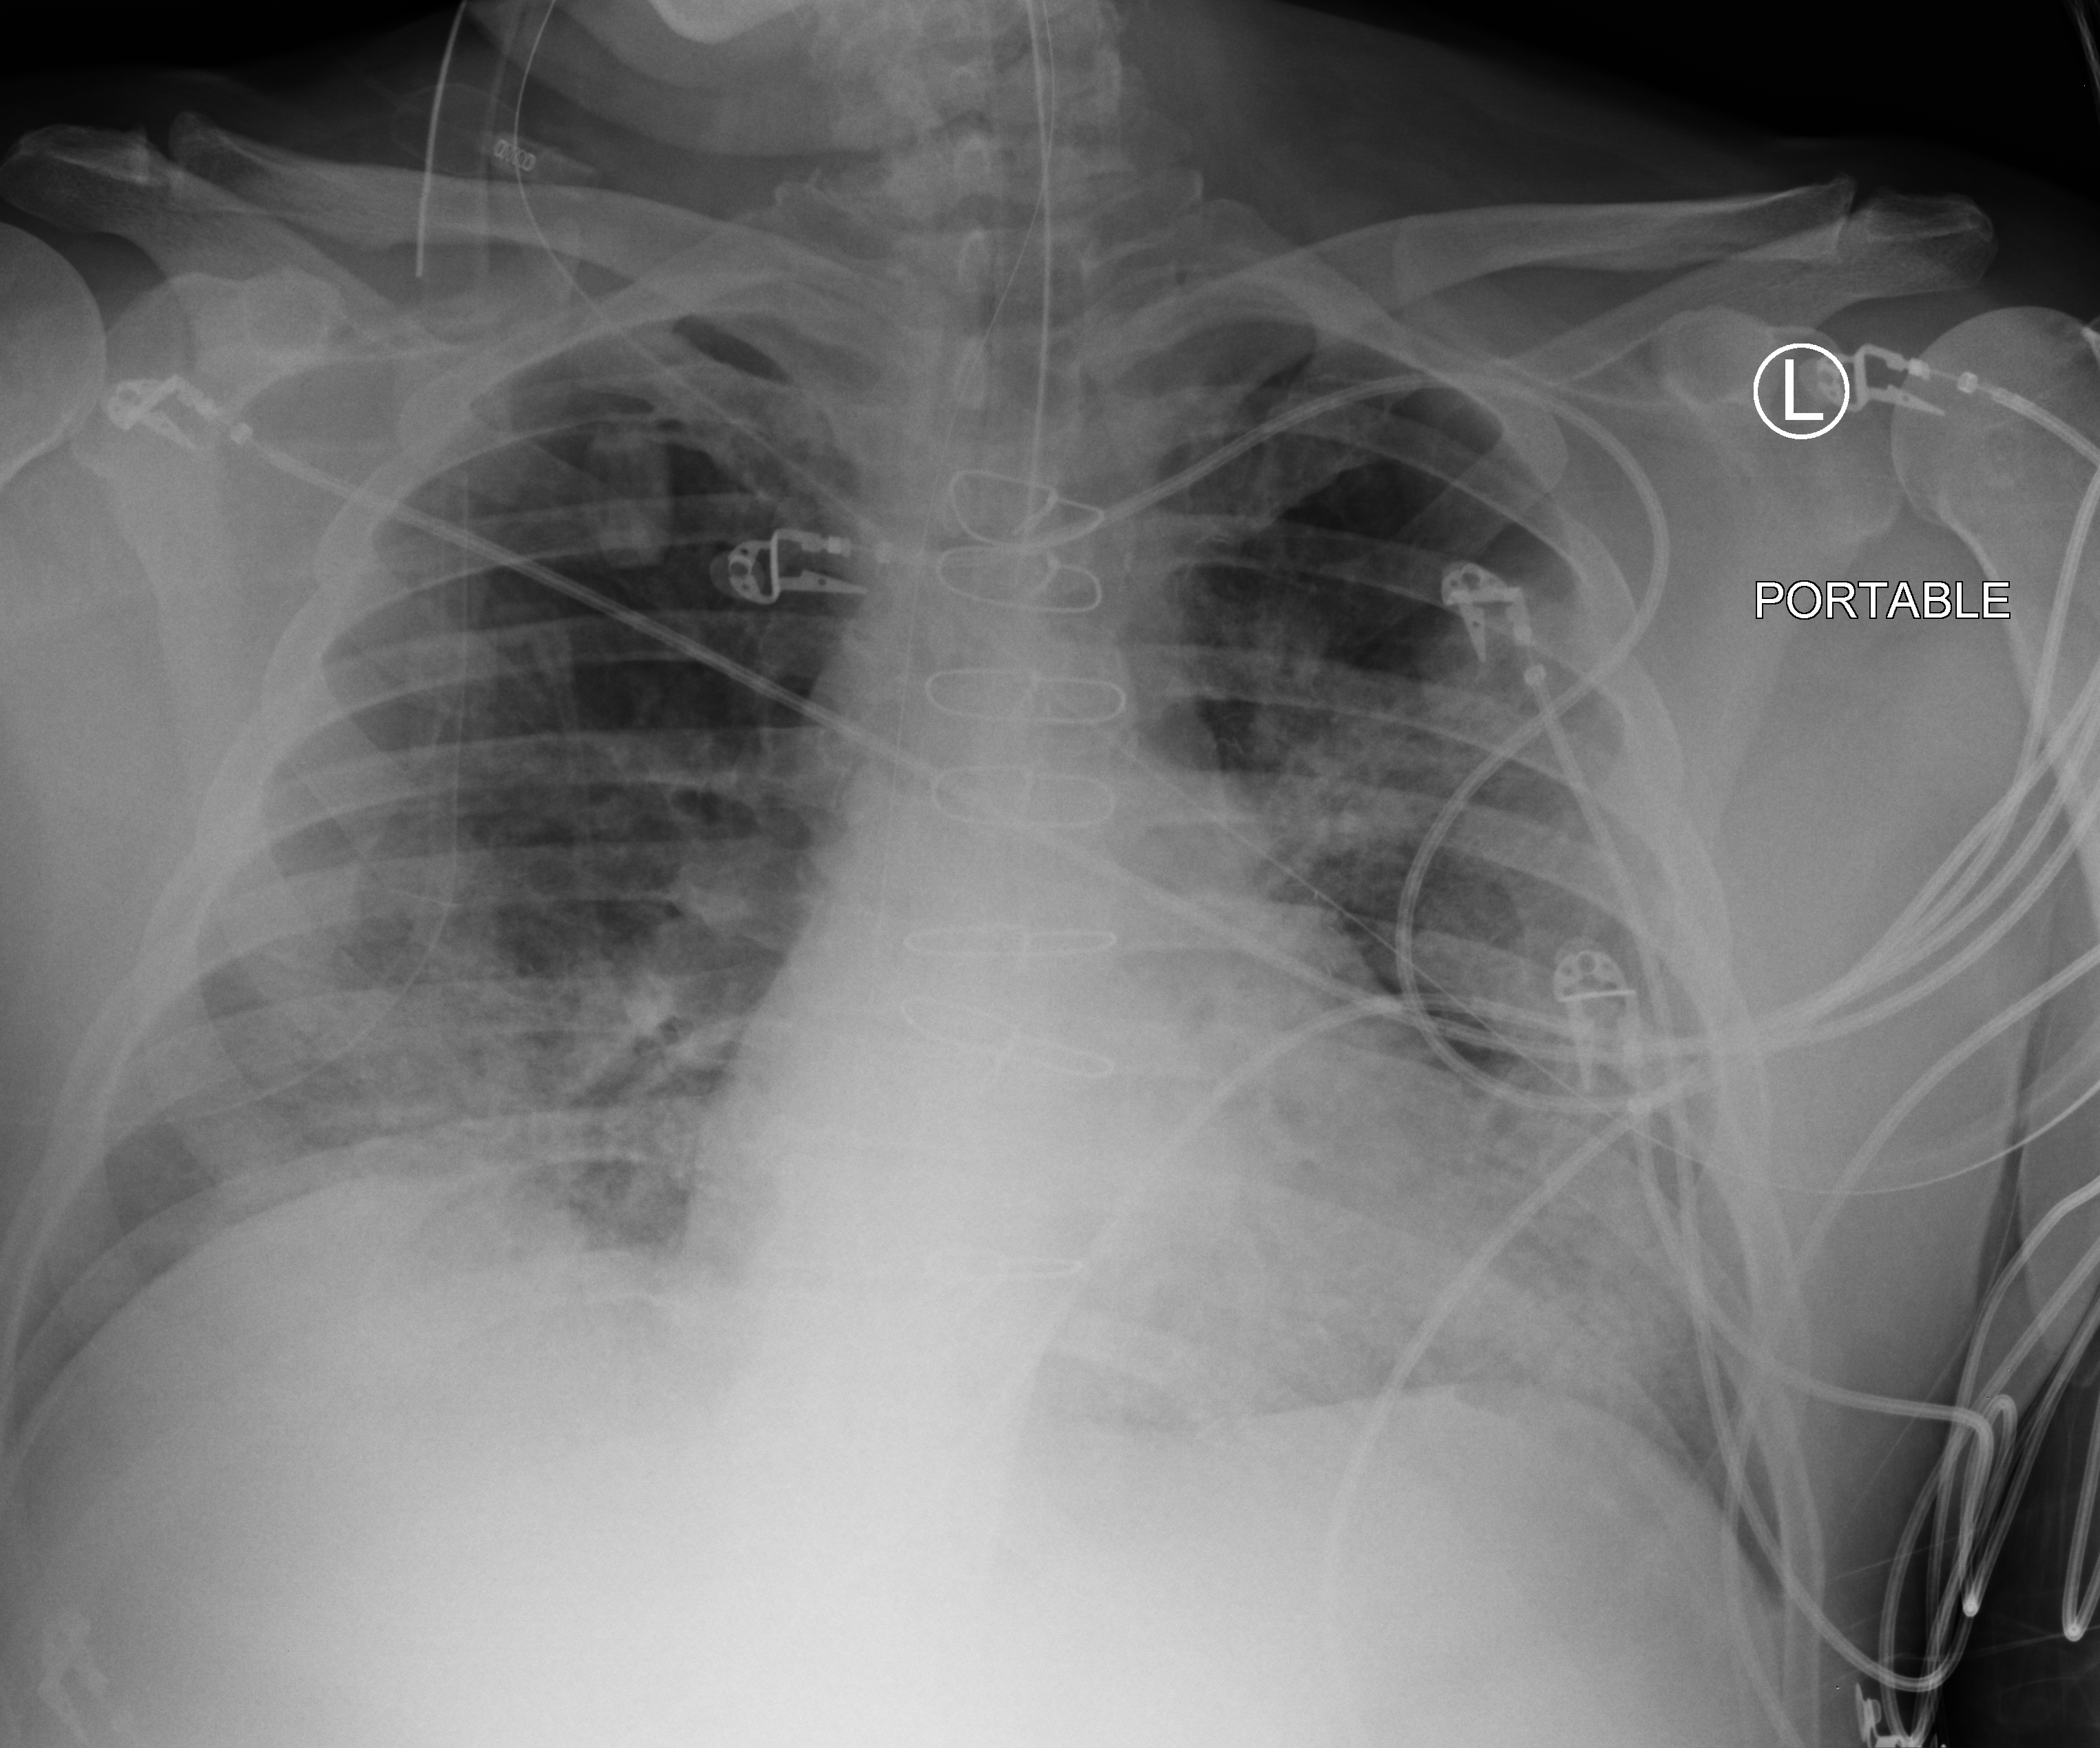
Portable chest radiograph, anteroposterior (AP) projection. Patient hospitalised with COVID-19; male, aged 60–74 years.
Admission-level facts for this patient (not findings on this image; timing relative to this image not recorded):
- chronic kidney disease (admission record): no
- mechanically ventilated during this hospital stay: yes